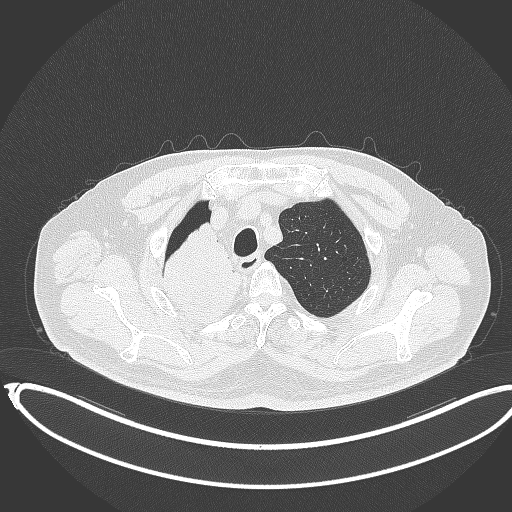
Chest CT, one axial slice. Position 312 of 403 along the scan axis. Reconstruction kernel B70f. 120 kVp. Lung window (W 1500 / L -600 HU). 512 × 512 image matrix. Patient: male, 68 years. Case-level facts recorded for this patient, not image findings: clinical TNM (as recorded): T2a N0 M0.
Annotated regions visible in this slice (bounding box drawn by a radiologist):
- lung tumour (recorded histology: adenocarcinoma): bounding box [x1, y1, x2, y2] px = [146, 222, 245, 325]